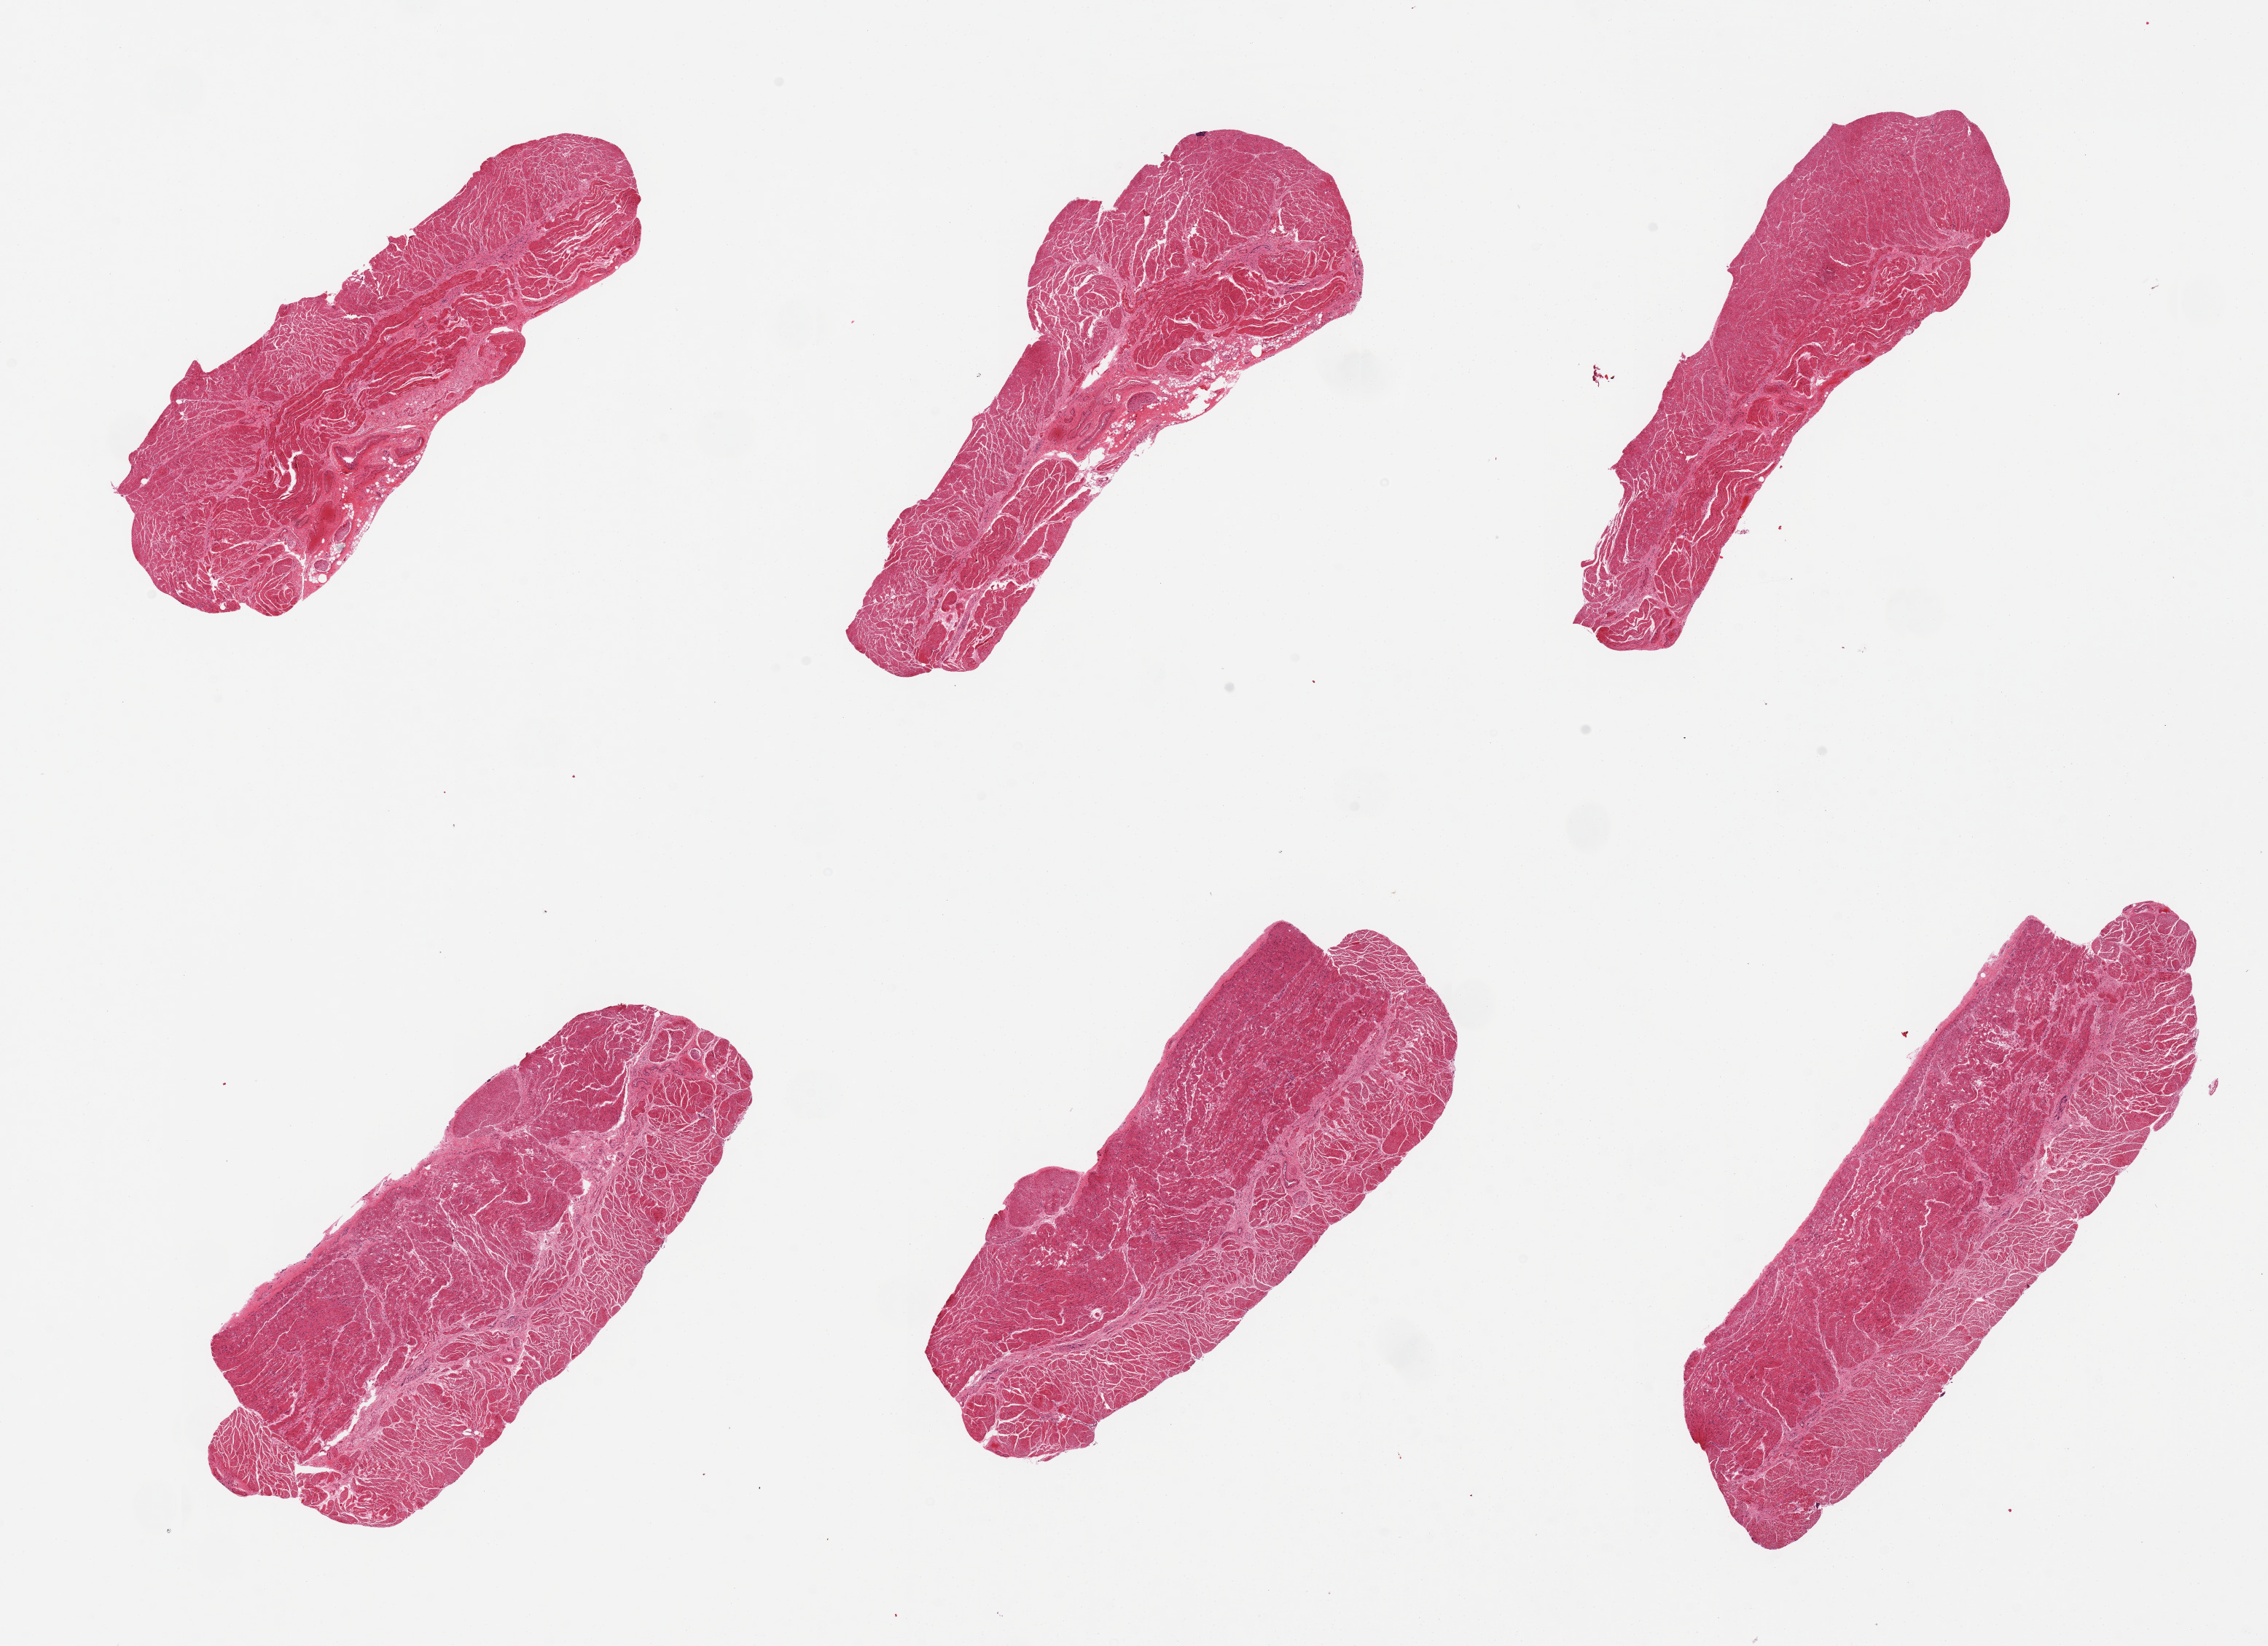
Haematoxylin and eosin whole-slide image, brightfield — a low-resolution overview of the entire scanned area, about 24.6 x 17.9 mm. PAXgene-fixed, paraffin-embedded tissue. Section of esophageal muscle (target tissue). Tissue donor sample. Donor: female.
* reviewer comment on this tissue sample: 6 pieces; well trimmed muscle